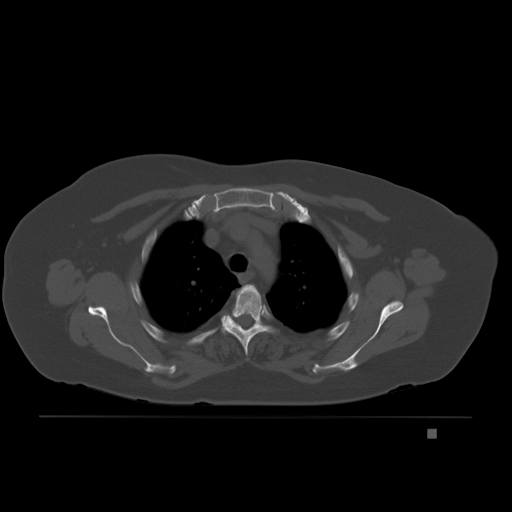
CT including the spine, one axial slice; slice 159 of 221 in the series (ordered by position); bone window (W 1800 / L 400 HU); 512 × 512 image matrix. Patient: female, 63 years. Case-level facts recorded for this patient, not image findings: primary cancer: breast.
Structures marked on this image (semi-automatic segmentation, software-assisted and operator-edited):
- T3 vertebra: box from (x=222, y=285) to (x=269, y=356) px